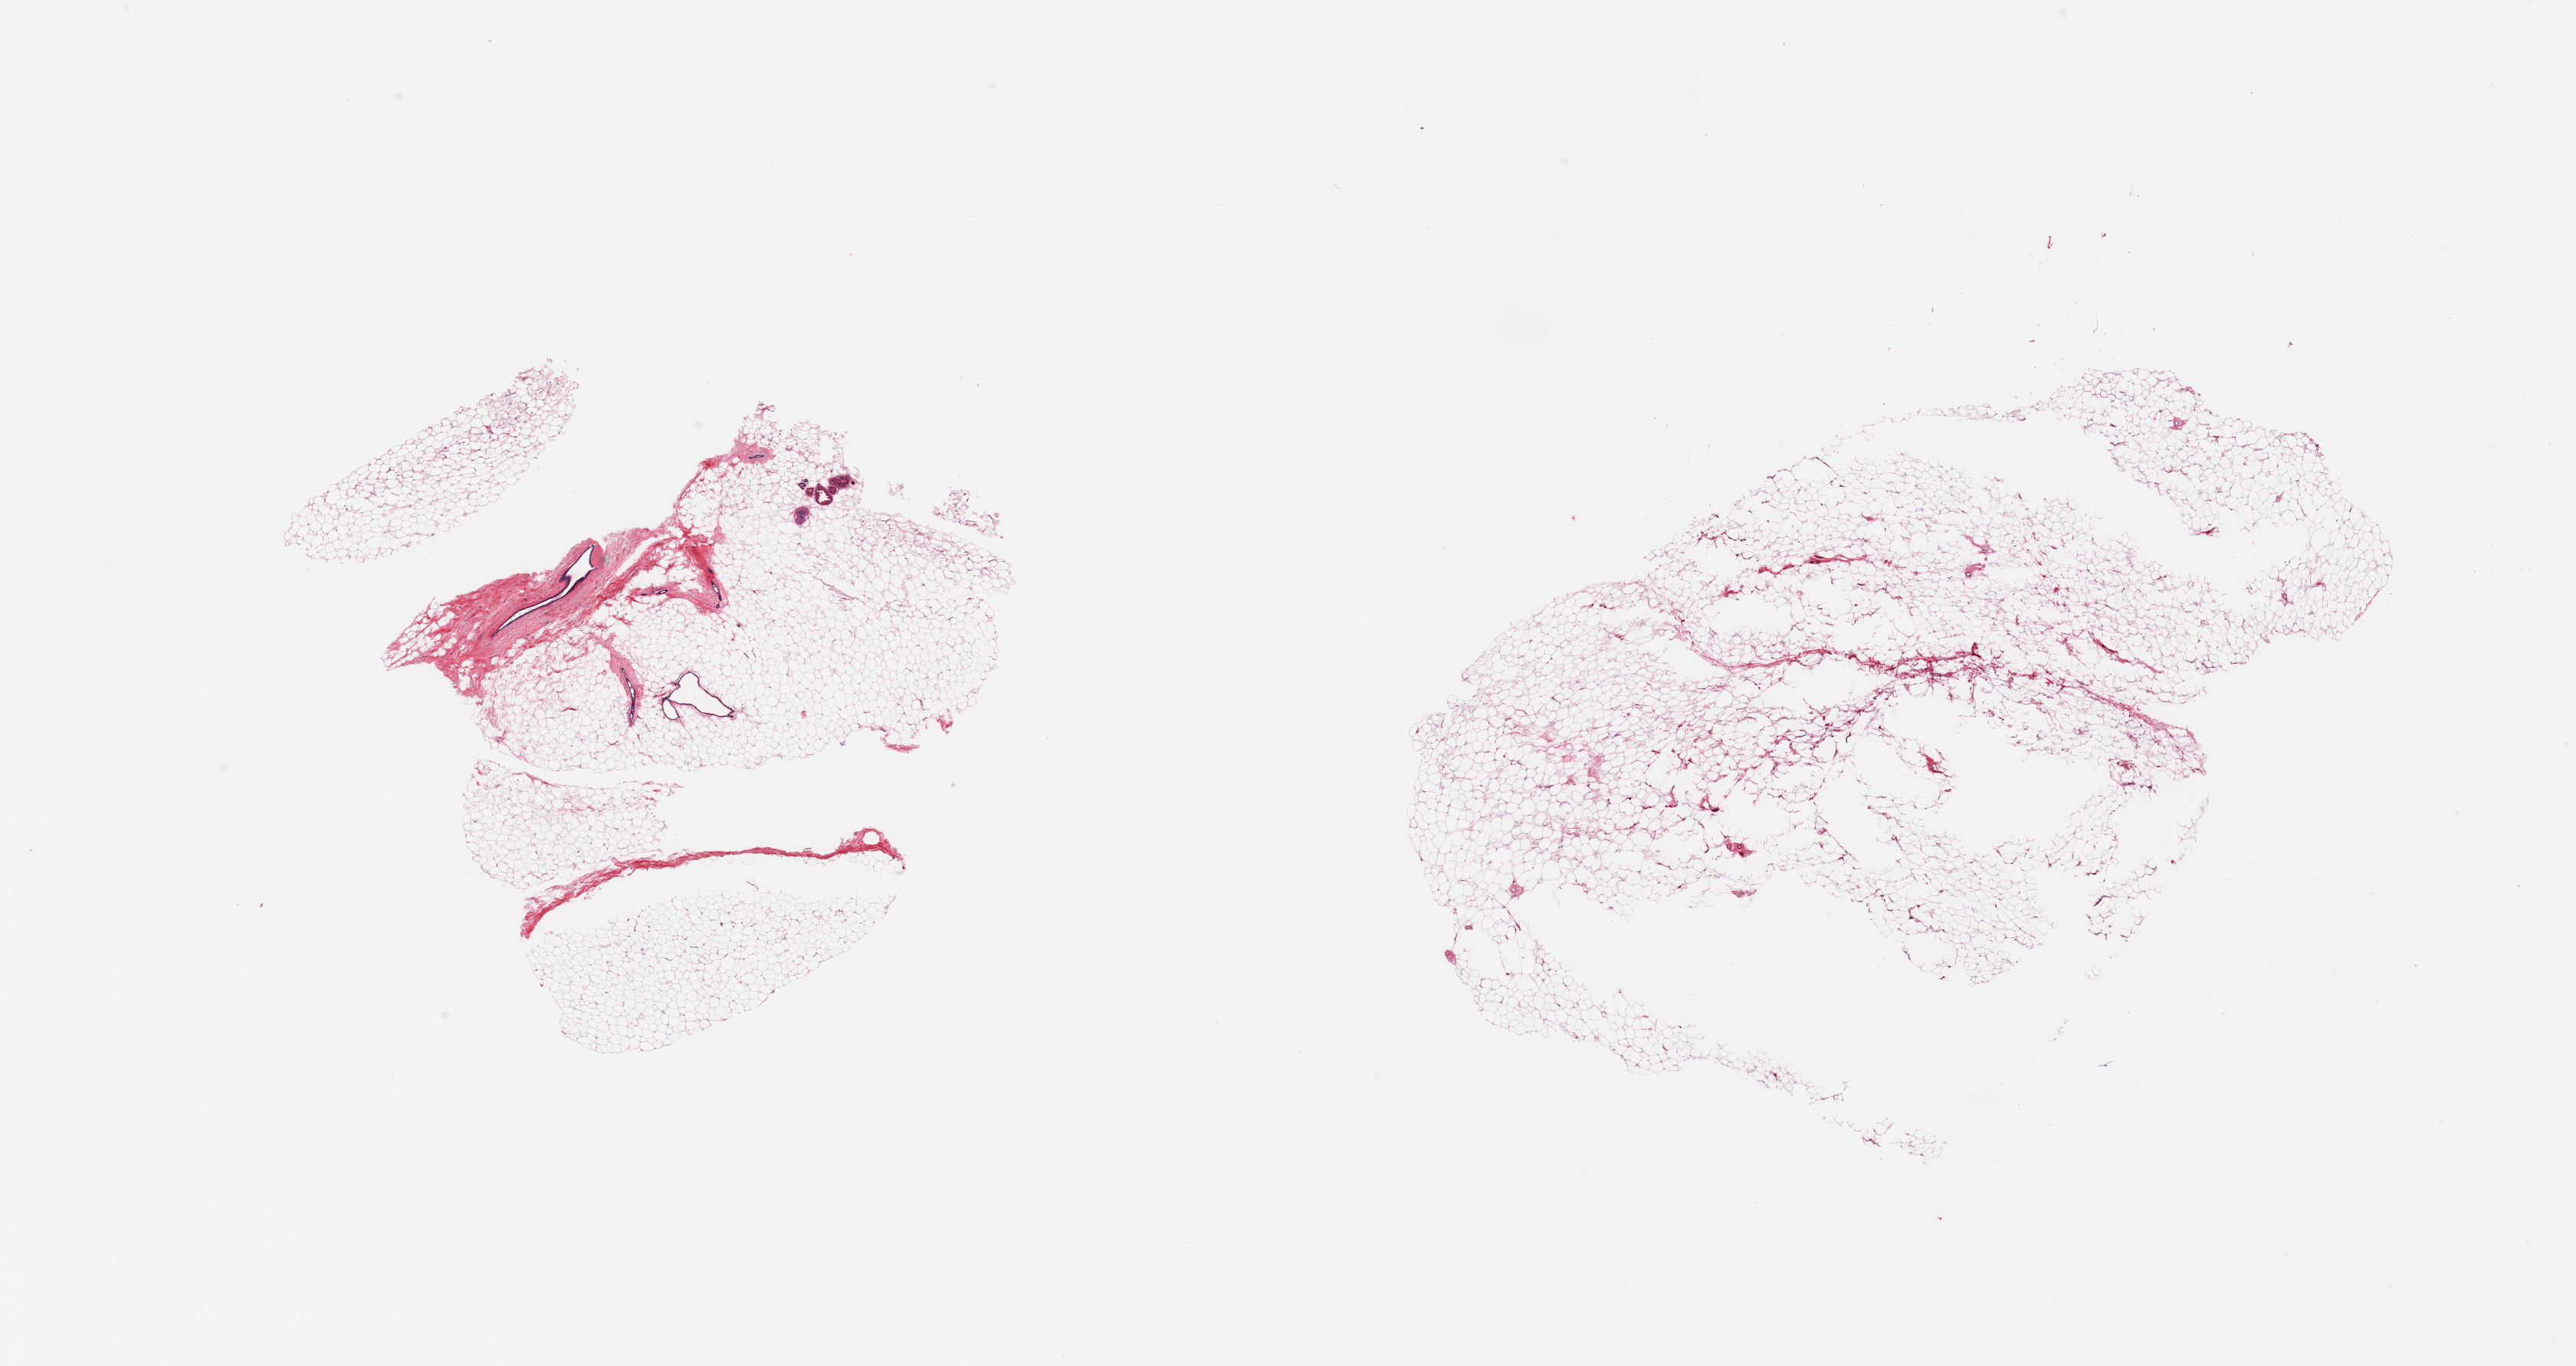
Digitized haematoxylin and eosin-stained section — a low-resolution overview of the entire scanned area, about 26.6 x 14.1 mm. PAXgene-fixed, paraffin-embedded tissue. Section of breast (target tissue). Tissue donor sample.
• review note (as recorded): 2 pieces, mainly adipose tissue; trace ductal elements with focal apocrine metaplasia (dleineated)